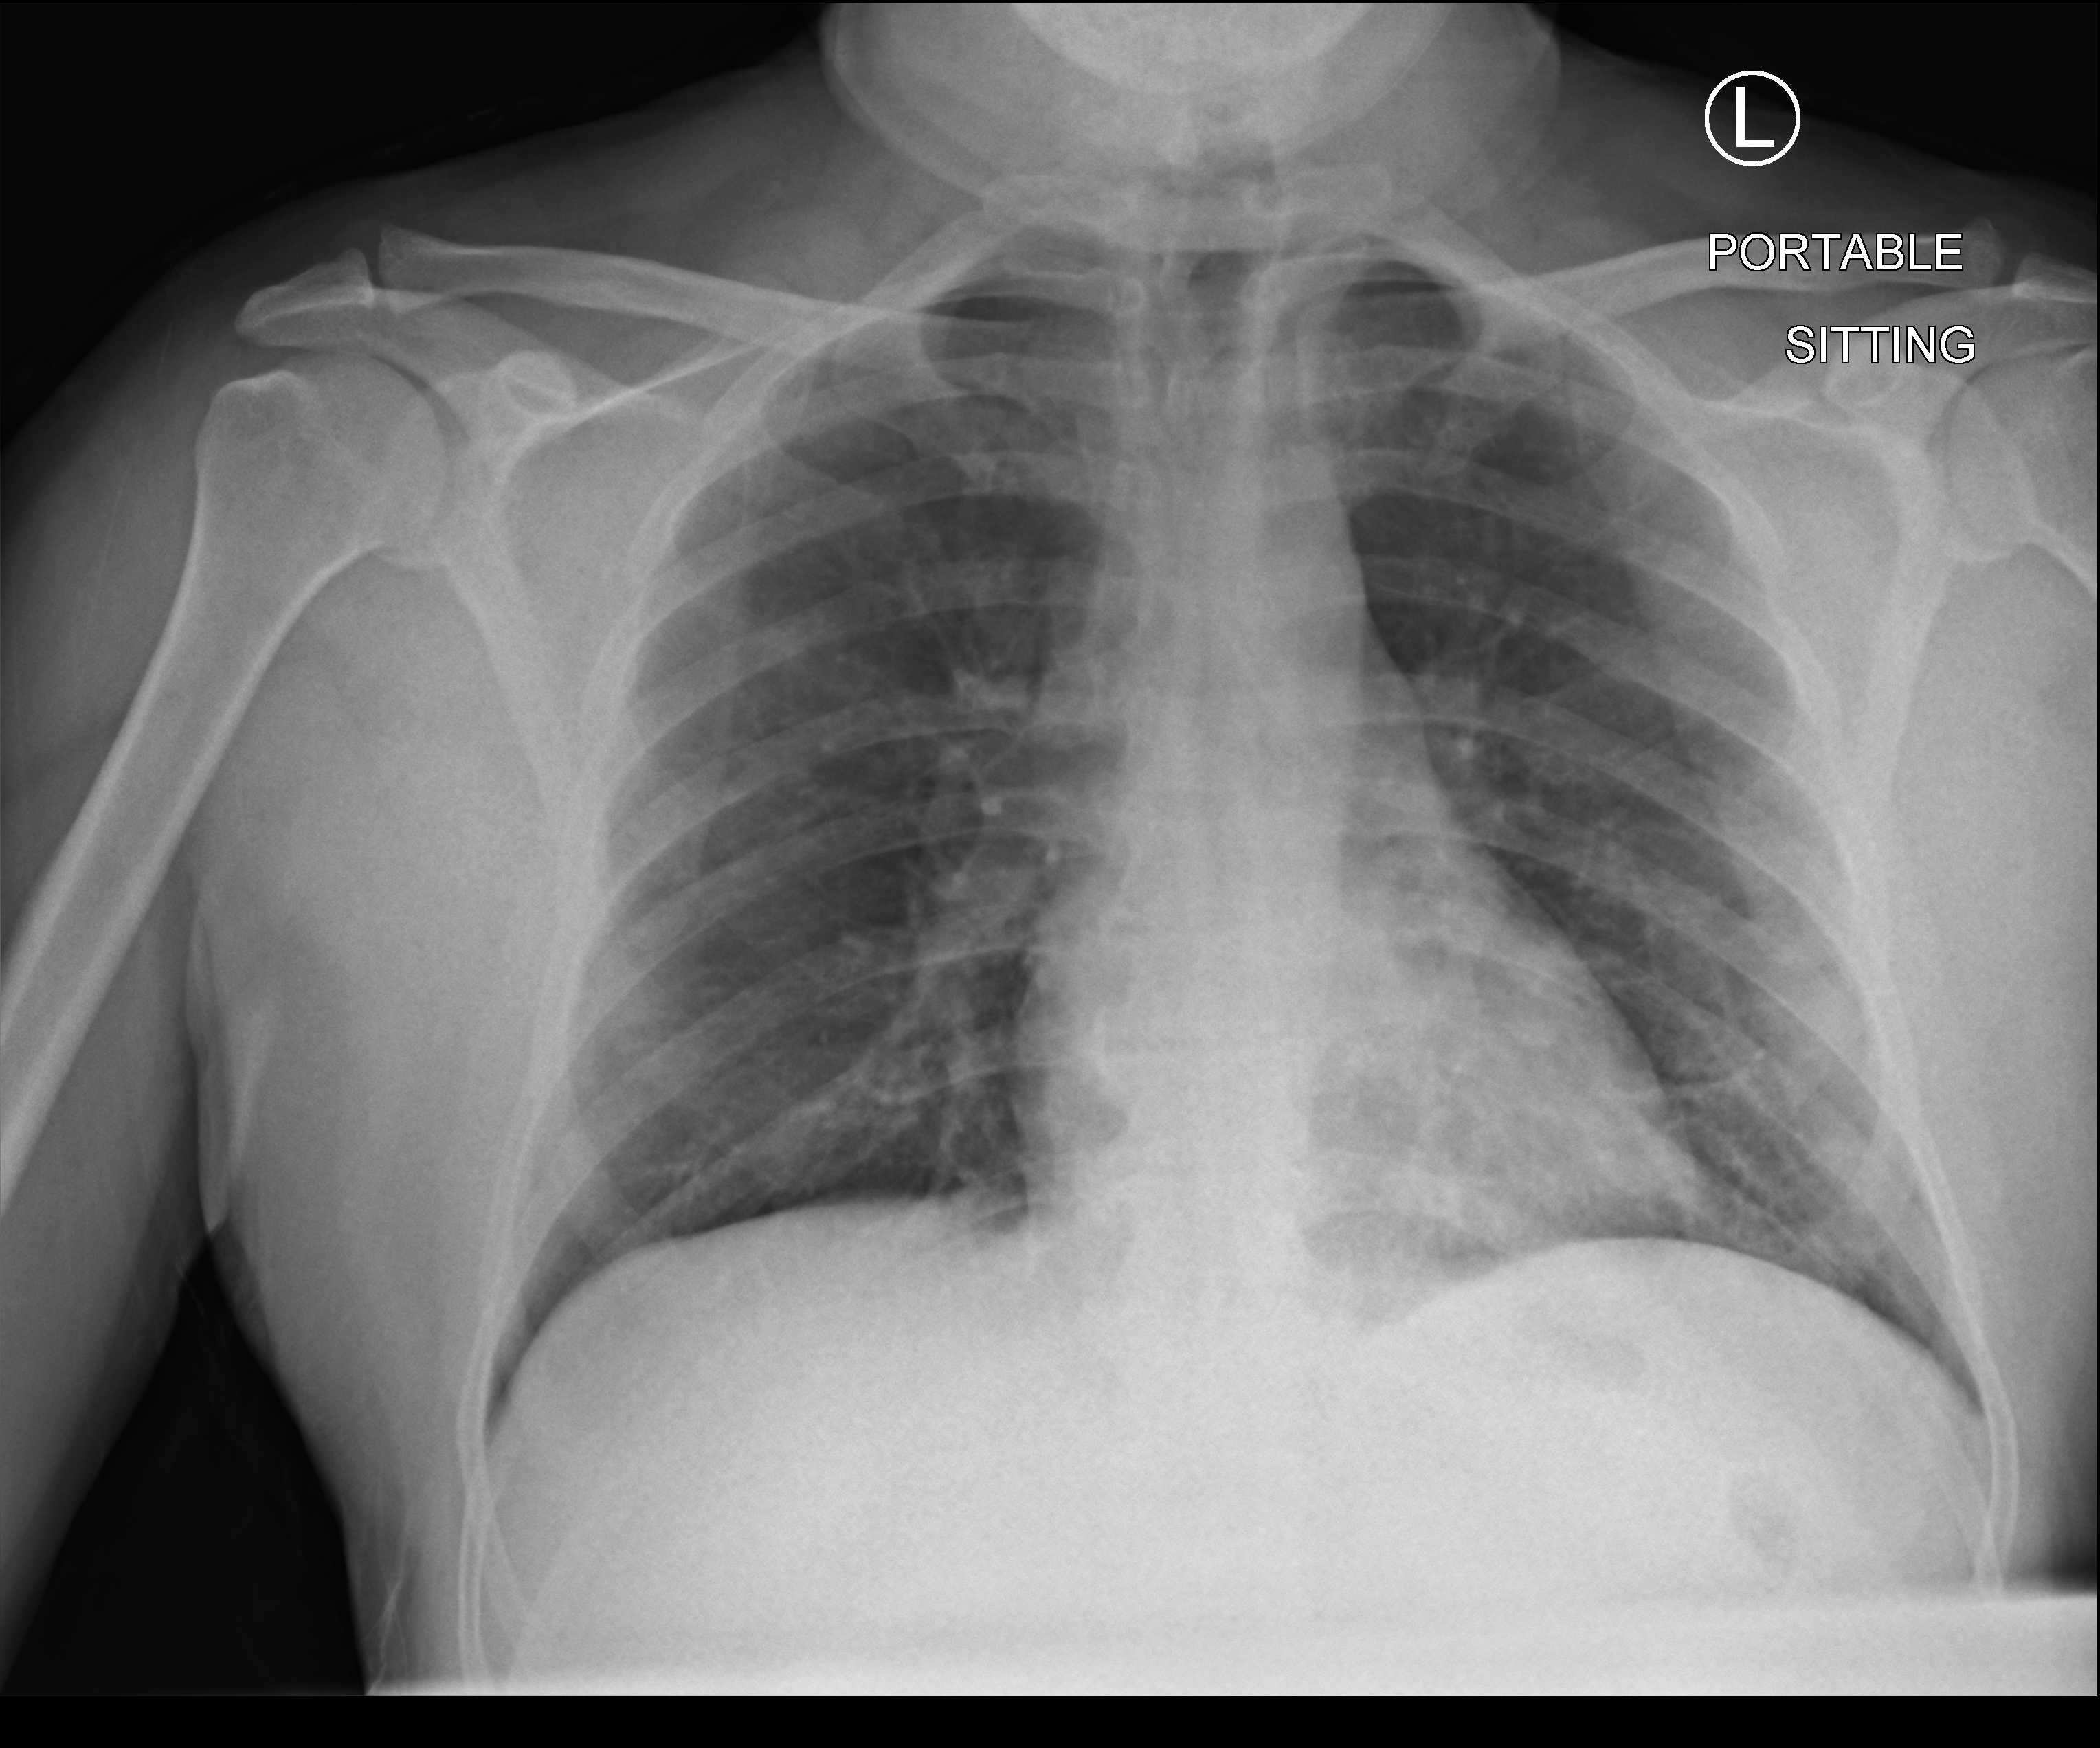
Bedside chest radiograph (computed radiography), anteroposterior (AP) projection. Male patient hospitalised with COVID-19, age 18–59 years.
Admission-level facts for this patient (not findings on this image; timing relative to this image not recorded):
- diabetes (admission record): no